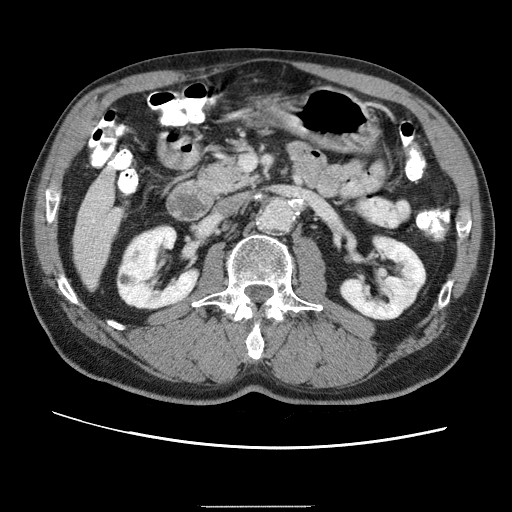
Contrast-enhanced abdominal CT (liver protocol), one axial slice. Slice 9 of 75 in the series (ordered by position). Reconstruction kernel STANDARD. 120 kVp. One of 2 acquisitions stored at this slice position. Soft-tissue window (W 400 / L 40 HU). 2.5 mm slice thickness. 512 × 512 image matrix, field of view 360 × 360 mm. From the clinical record (not read from this slice): diagnosis: hepatocellular carcinoma (patient treated with transarterial chemoembolisation; whether this scan precedes or follows treatment is not stated here); TNM stage (as recorded): Stage-II; Child-Pugh class: A; tumour differentiation: well differentiated; tumour nodularity: multinodular.
Outlined on this slice (semi-automatic segmentation, software-assisted and operator-edited):
- liver parenchyma outside the tumour (the mass and vessels are separate outlines, so this box may not span the whole liver): bounding box <74,170,109,274> (left, top, right, bottom; pixels)
- liver vessels: <82,173,104,240>